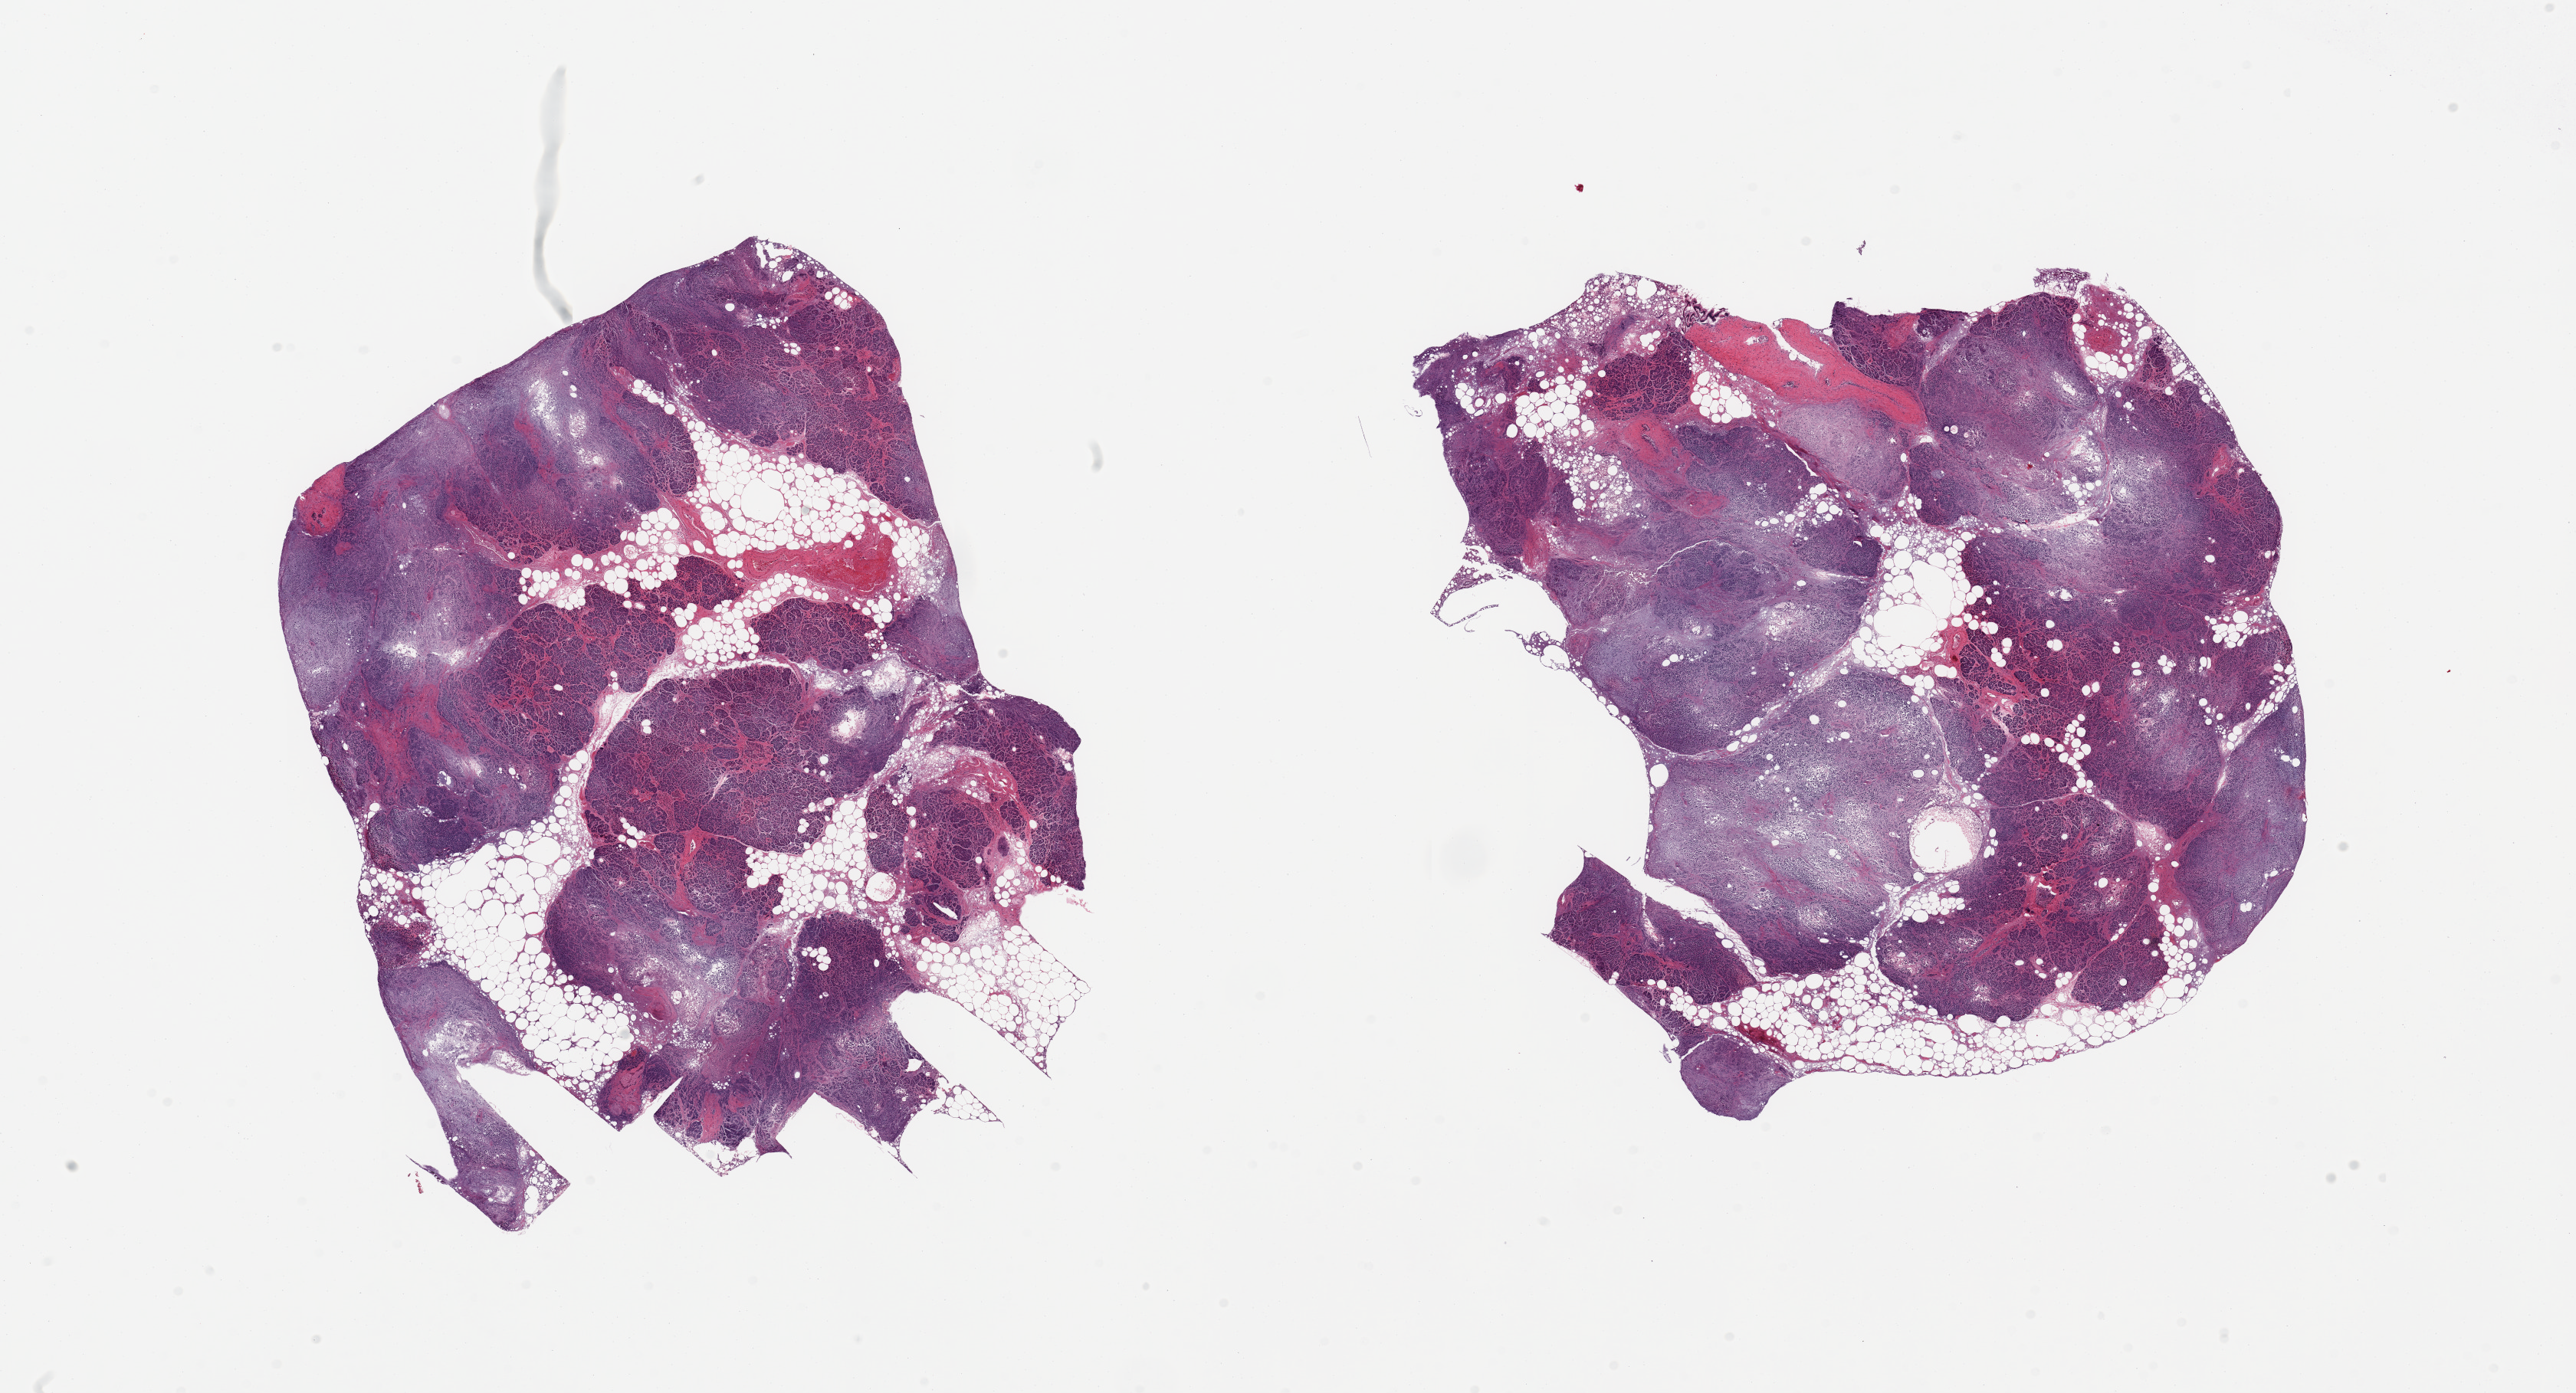
Hematoxylin and eosin (H&E) whole-slide image — whole scanned area (about 26.6 x 14.4 mm, from a 20x scan) shown as a low-resolution overview. PAXgene-fixed paraffin-embedded (PFPE) section. Section of pancreas (target tissue). Tissue donor sample. Donor sex: male.
Reviewer comment on this tissue sample: 2 pieces; up to 20% internal and attached fat, severely autolyzed.